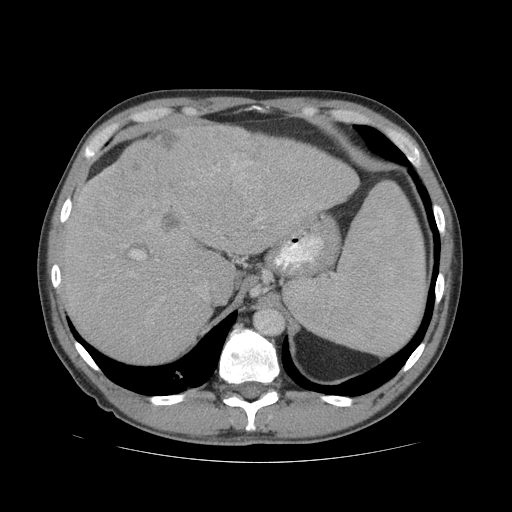
Contrast-enhanced abdominal CT (liver protocol), one axial slice; slice 52 of 81 in the series (ordered by position); reconstruction kernel STANDARD; soft-tissue window (W 400 / L 40 HU); 512 × 512 image matrix, field of view 400 × 400 mm. Case-level facts recorded for this patient, not image findings: diagnosis: hepatocellular carcinoma (patient treated with transarterial chemoembolisation; whether this scan precedes or follows treatment is not stated here); TNM stage (as recorded): Stage-IVB; Child-Pugh class: B; tumour nodularity: multinodular.
Outlined on this slice (semi-automatic segmentation, software-assisted and operator-edited):
- liver parenchyma outside the tumour (the mass and vessels are separate outlines, so this box may not span the whole liver): bounding box <60,124,358,363> (left, top, right, bottom; pixels)
- mass: <87,125,250,243>
- liver vessels: <79,161,297,272>